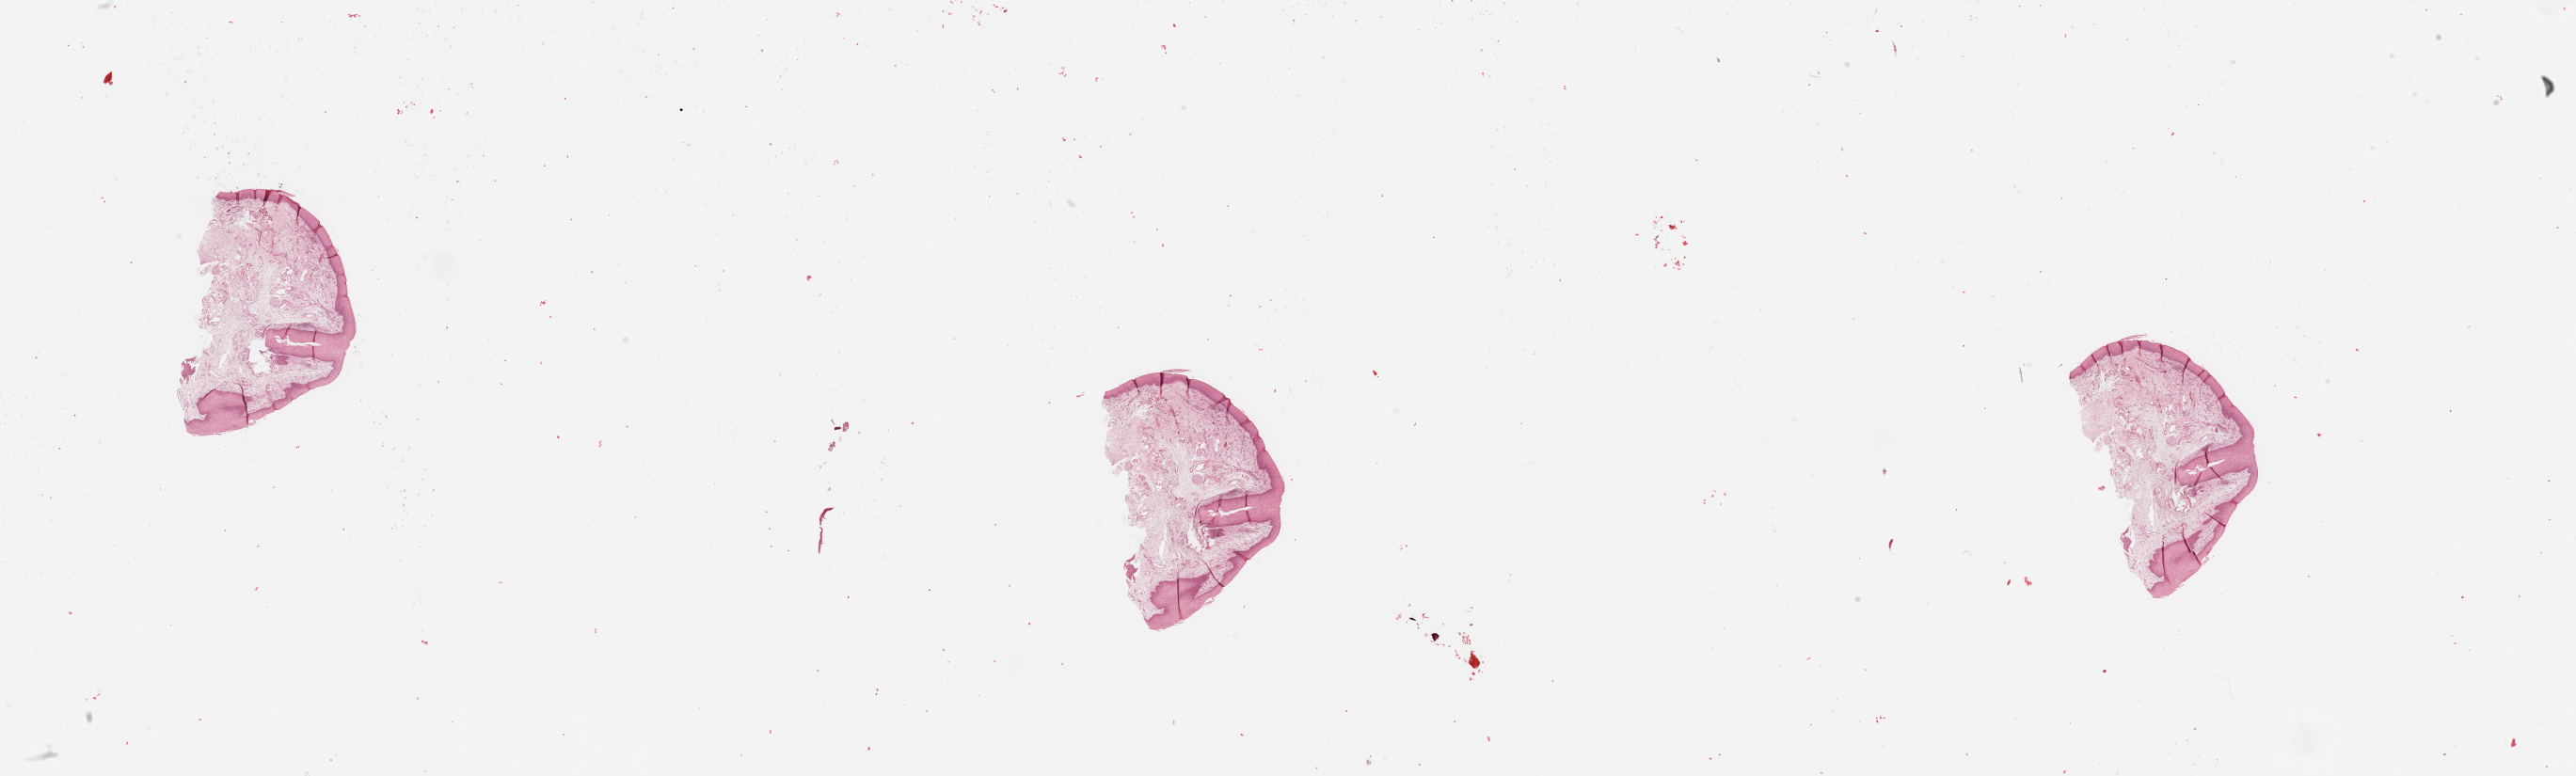
Whole-slide histology image, H&E, shown as a low-resolution overview of the whole scanned area (about 43.3 x 13.1 mm, slide scanned at 20x), normal (non-tumour) tissue sample, head and neck. Male, 62 y/o.
This section: normal (non-tumour) tissue from the same patient. Patient diagnosis: Squamous cell carcinoma, NOS (larynx, NOS).